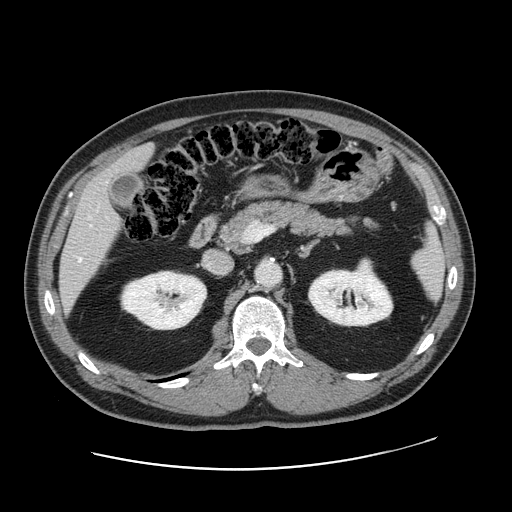
Contrast-enhanced abdominal CT, one axial slice; position 84 of 178 along the scan axis; 120 kVp; intravenous contrast given; soft-tissue window (W 400 / L 40 HU); 2.5 mm slice thickness; 512 × 512 image matrix, field of view 403 × 403 mm. Male patient, age 63 years. Case-level facts recorded for this patient, not image findings: diagnosis: colorectal cancer liver metastases, imaged before liver resection; multiple liver metastases: yes; largest metastasis: 8 cm; chemotherapy before resection: no.
Annotated regions visible in this slice (manually delineated by an expert):
- hepatic veins: bounding box <79,225,91,261> (left, top, right, bottom; pixels)
- liver: <61,146,153,305>
- planned liver remnant (the part of the liver to remain after resection): <111,146,153,173>